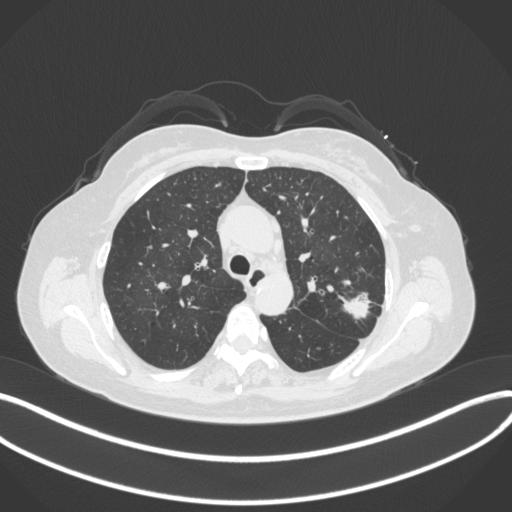
Chest CT, one axial slice; position 239 of 330 along the scan axis; reconstruction kernel B31f; 120 kVp; lung window (W 1500 / L -600 HU); 1 mm slice thickness; 512 × 512 image matrix, field of view 400 × 400 mm. Female patient, age 60 years. Case-level facts recorded for this patient, not image findings: clinical TNM (as recorded): T1c N0 M0.
Structures marked on this image (rectangle marked by the reading radiologist):
- lung tumour (recorded histology: adenocarcinoma): bounding box (x1, y1, x2, y2) in pixels: (340, 282, 376, 324)